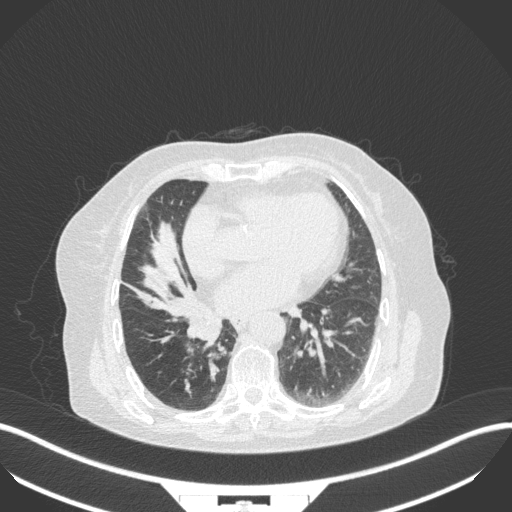
Chest CT, one axial slice; position 128 of 329 along the scan axis; lung window (W 1500 / L -600 HU); 1 mm slice thickness; 512 × 512 image matrix, field of view 400 × 400 mm. Female patient, age 75 years. Case-level facts recorded for this patient, not image findings: clinical TNM (as recorded): T1b N0 M1a; histopathological grade: G1.
Annotated regions visible in this slice (rectangle marked by the reading radiologist):
- lung tumour (recorded histology: squamous cell carcinoma): bounding box (x1, y1, x2, y2) in pixels: (182, 308, 226, 351)